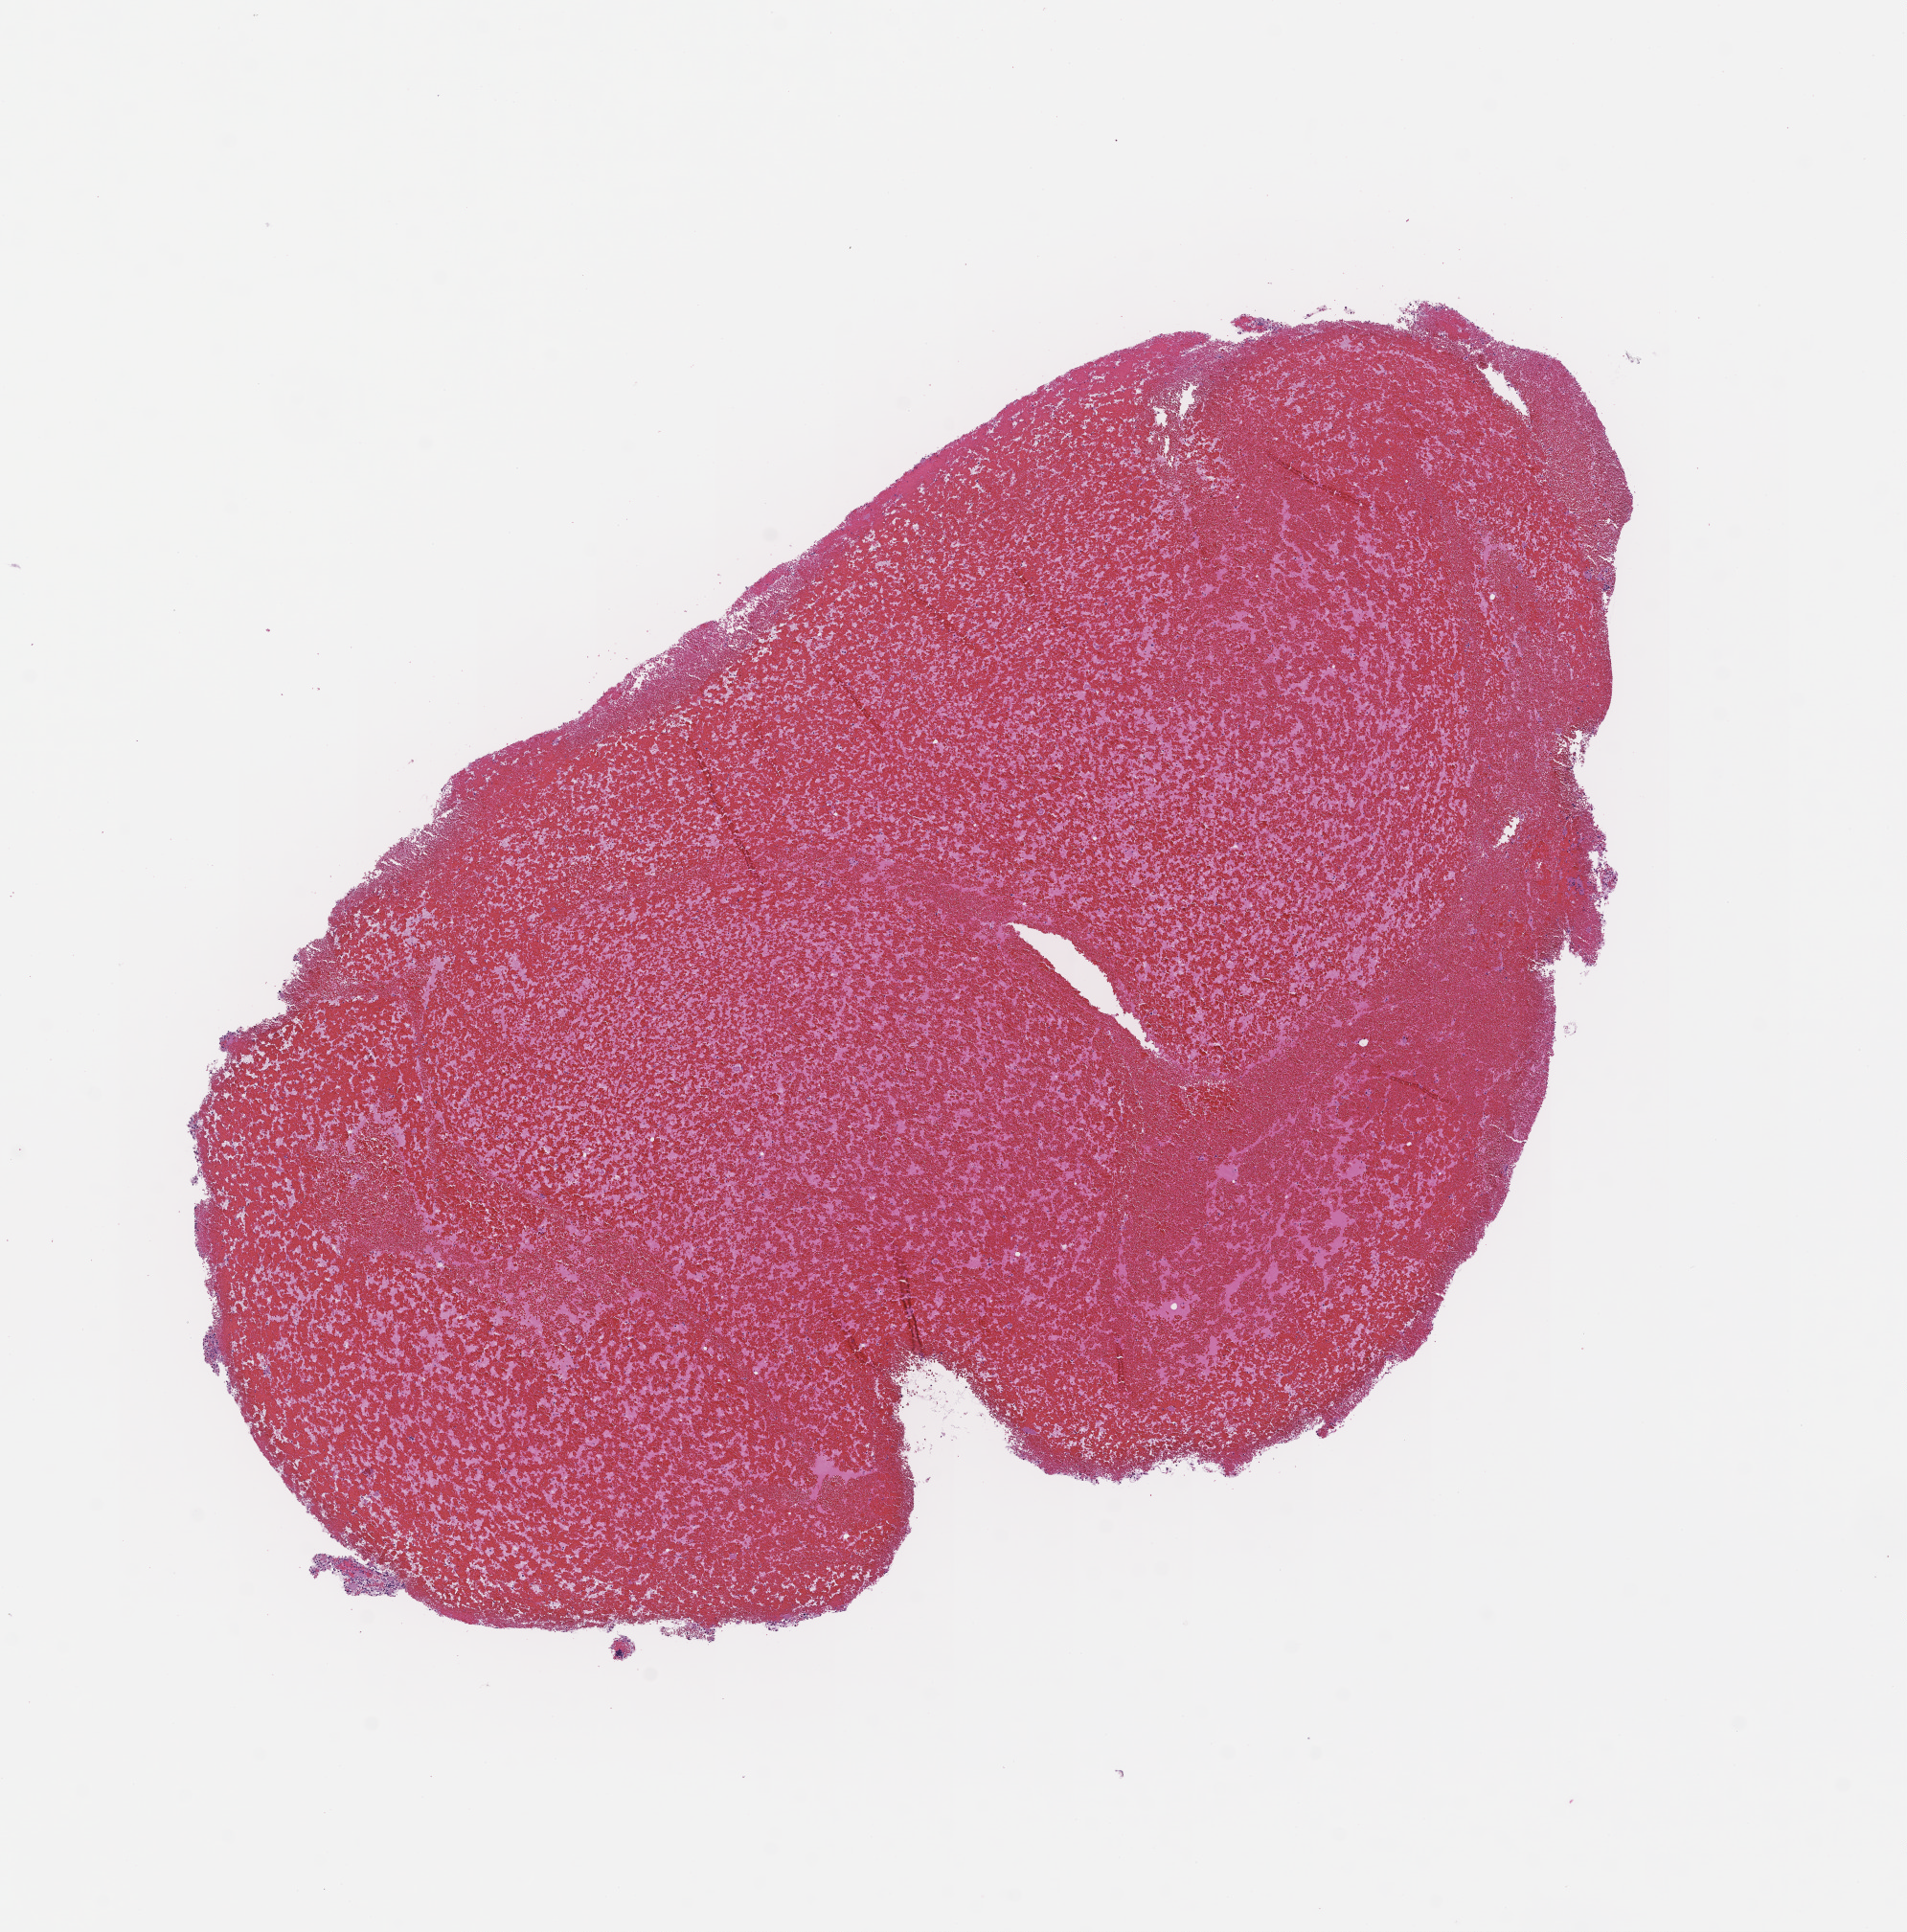
Haematoxylin and eosin whole-slide image — low-resolution overview of the scanned area, about 8.0 x 8.1 mm, formalin-fixed, paraffin-embedded (FFPE) tissue, site: bone marrow, archival tissue. Patient sex: male.
This section: primary tumour tissue. Diagnosis: Plasma Cell Myeloma.